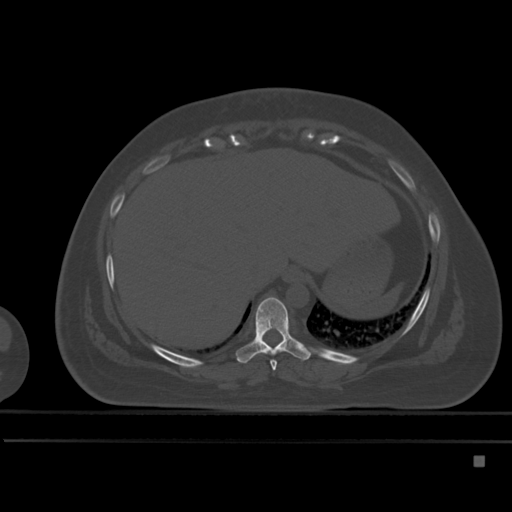
CT including the spine, one axial slice. Slice 264 of 495 in the series (ordered by position). Bone window (W 1800 / L 400 HU). 1.5 mm slice thickness. 512 × 512 image matrix, field of view 404 × 404 mm. Female patient, age 33 years. From the clinical record (not read from this slice): primary cancer: breast.
Annotated regions visible in this slice (semi-automatic segmentation, software-assisted and operator-edited):
- T8 vertebra: box from (x=270, y=360) to (x=277, y=370) px
- T9 vertebra: (x=236, y=297)–(x=311, y=364)